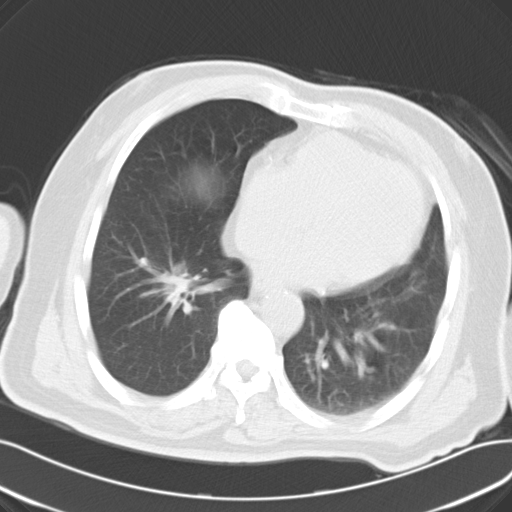
Chest CT, one axial slice; slice 14 of 30 in the series (ordered by position); reconstruction kernel B40f; lung window (W 1500 / L -600 HU); 10 mm slice thickness; 512 × 512 image matrix. Male patient, age 69 years. From the clinical record (not read from this slice): clinical TNM (as recorded): T1c N0 M0; histopathological grade: G2-3.
Outlined on this slice (bounding box drawn by a radiologist):
- lung tumour (recorded histology: adenocarcinoma): bounding box <161,258,186,309> (left, top, right, bottom; pixels)